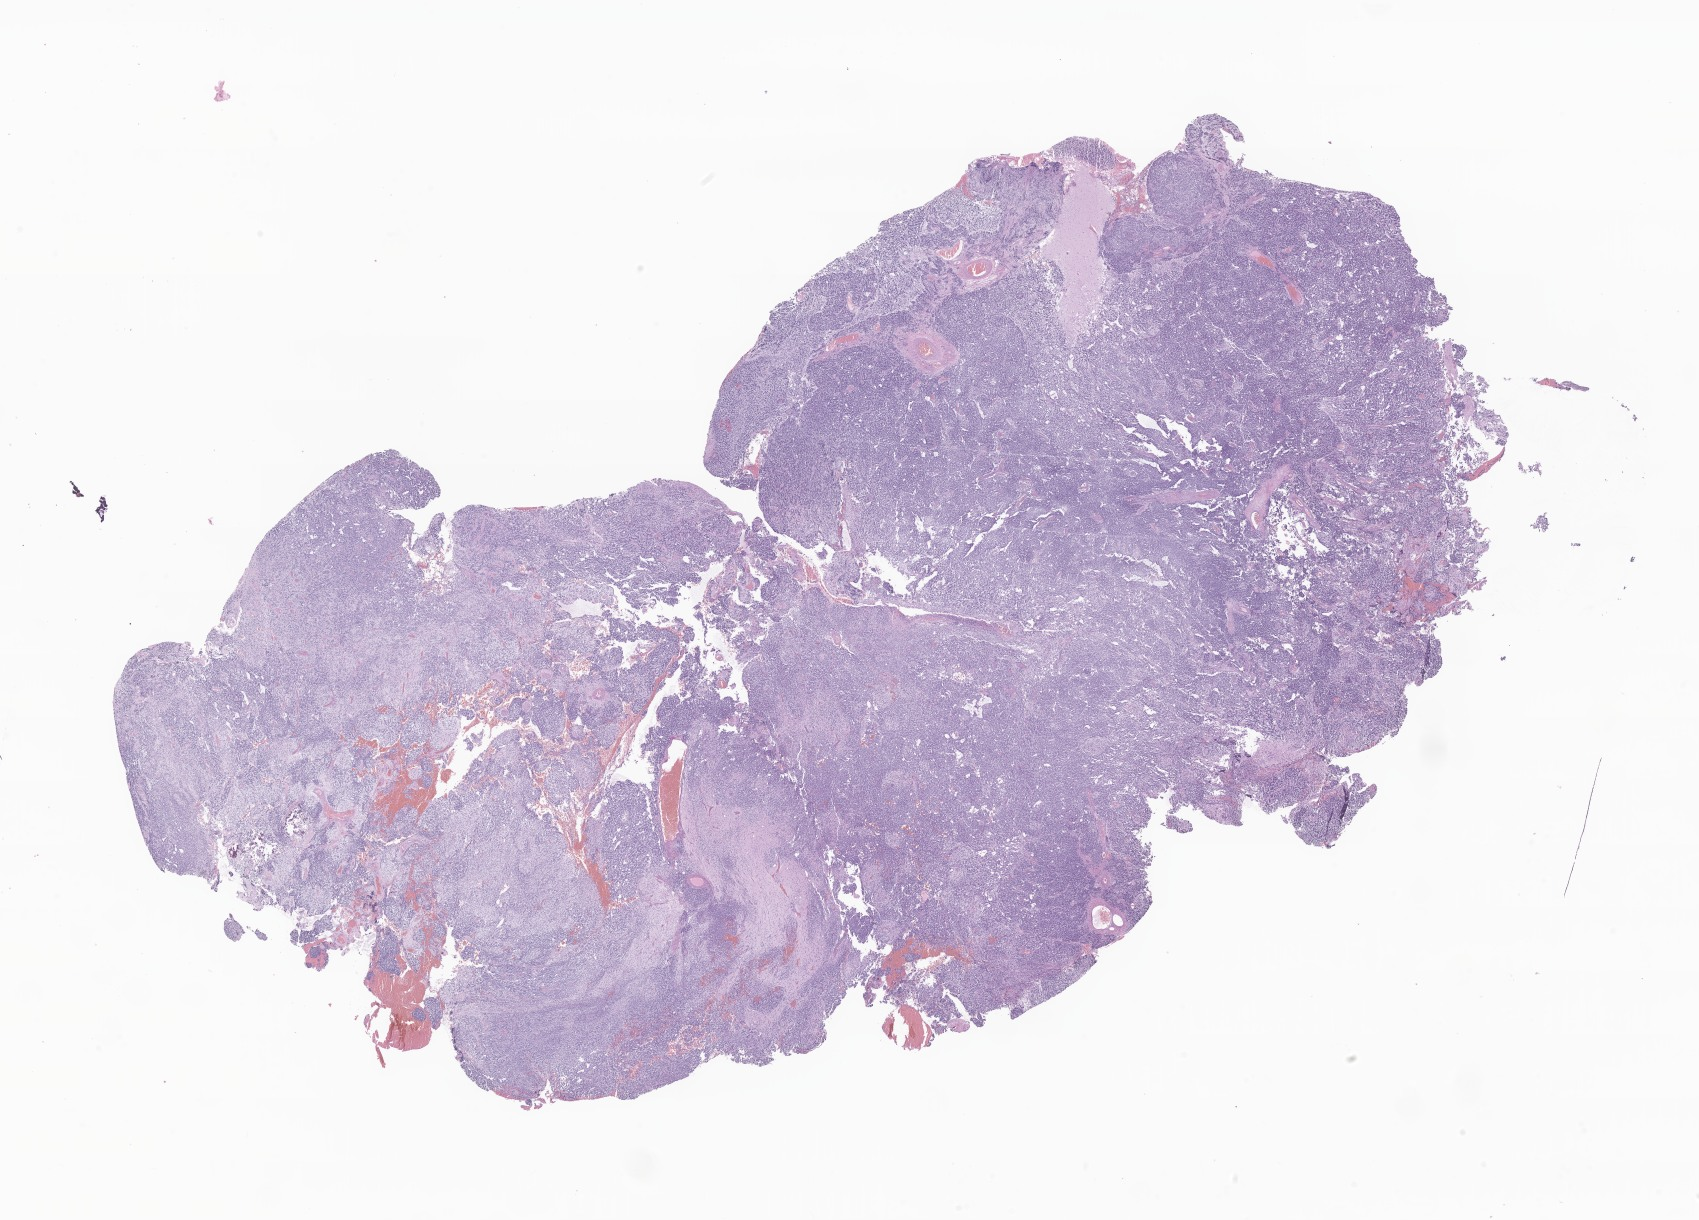
Whole-slide image, haematoxylin and eosin stain of tumor tissue from the brain, shown as a low-resolution overview of the whole scanned area (about 28.7 x 20.6 mm), formalin-fixed paraffin-embedded section. Patient: female, age 80 months (6 years 8 months).
Recorded diagnosis: Medulloblastoma, NOS.